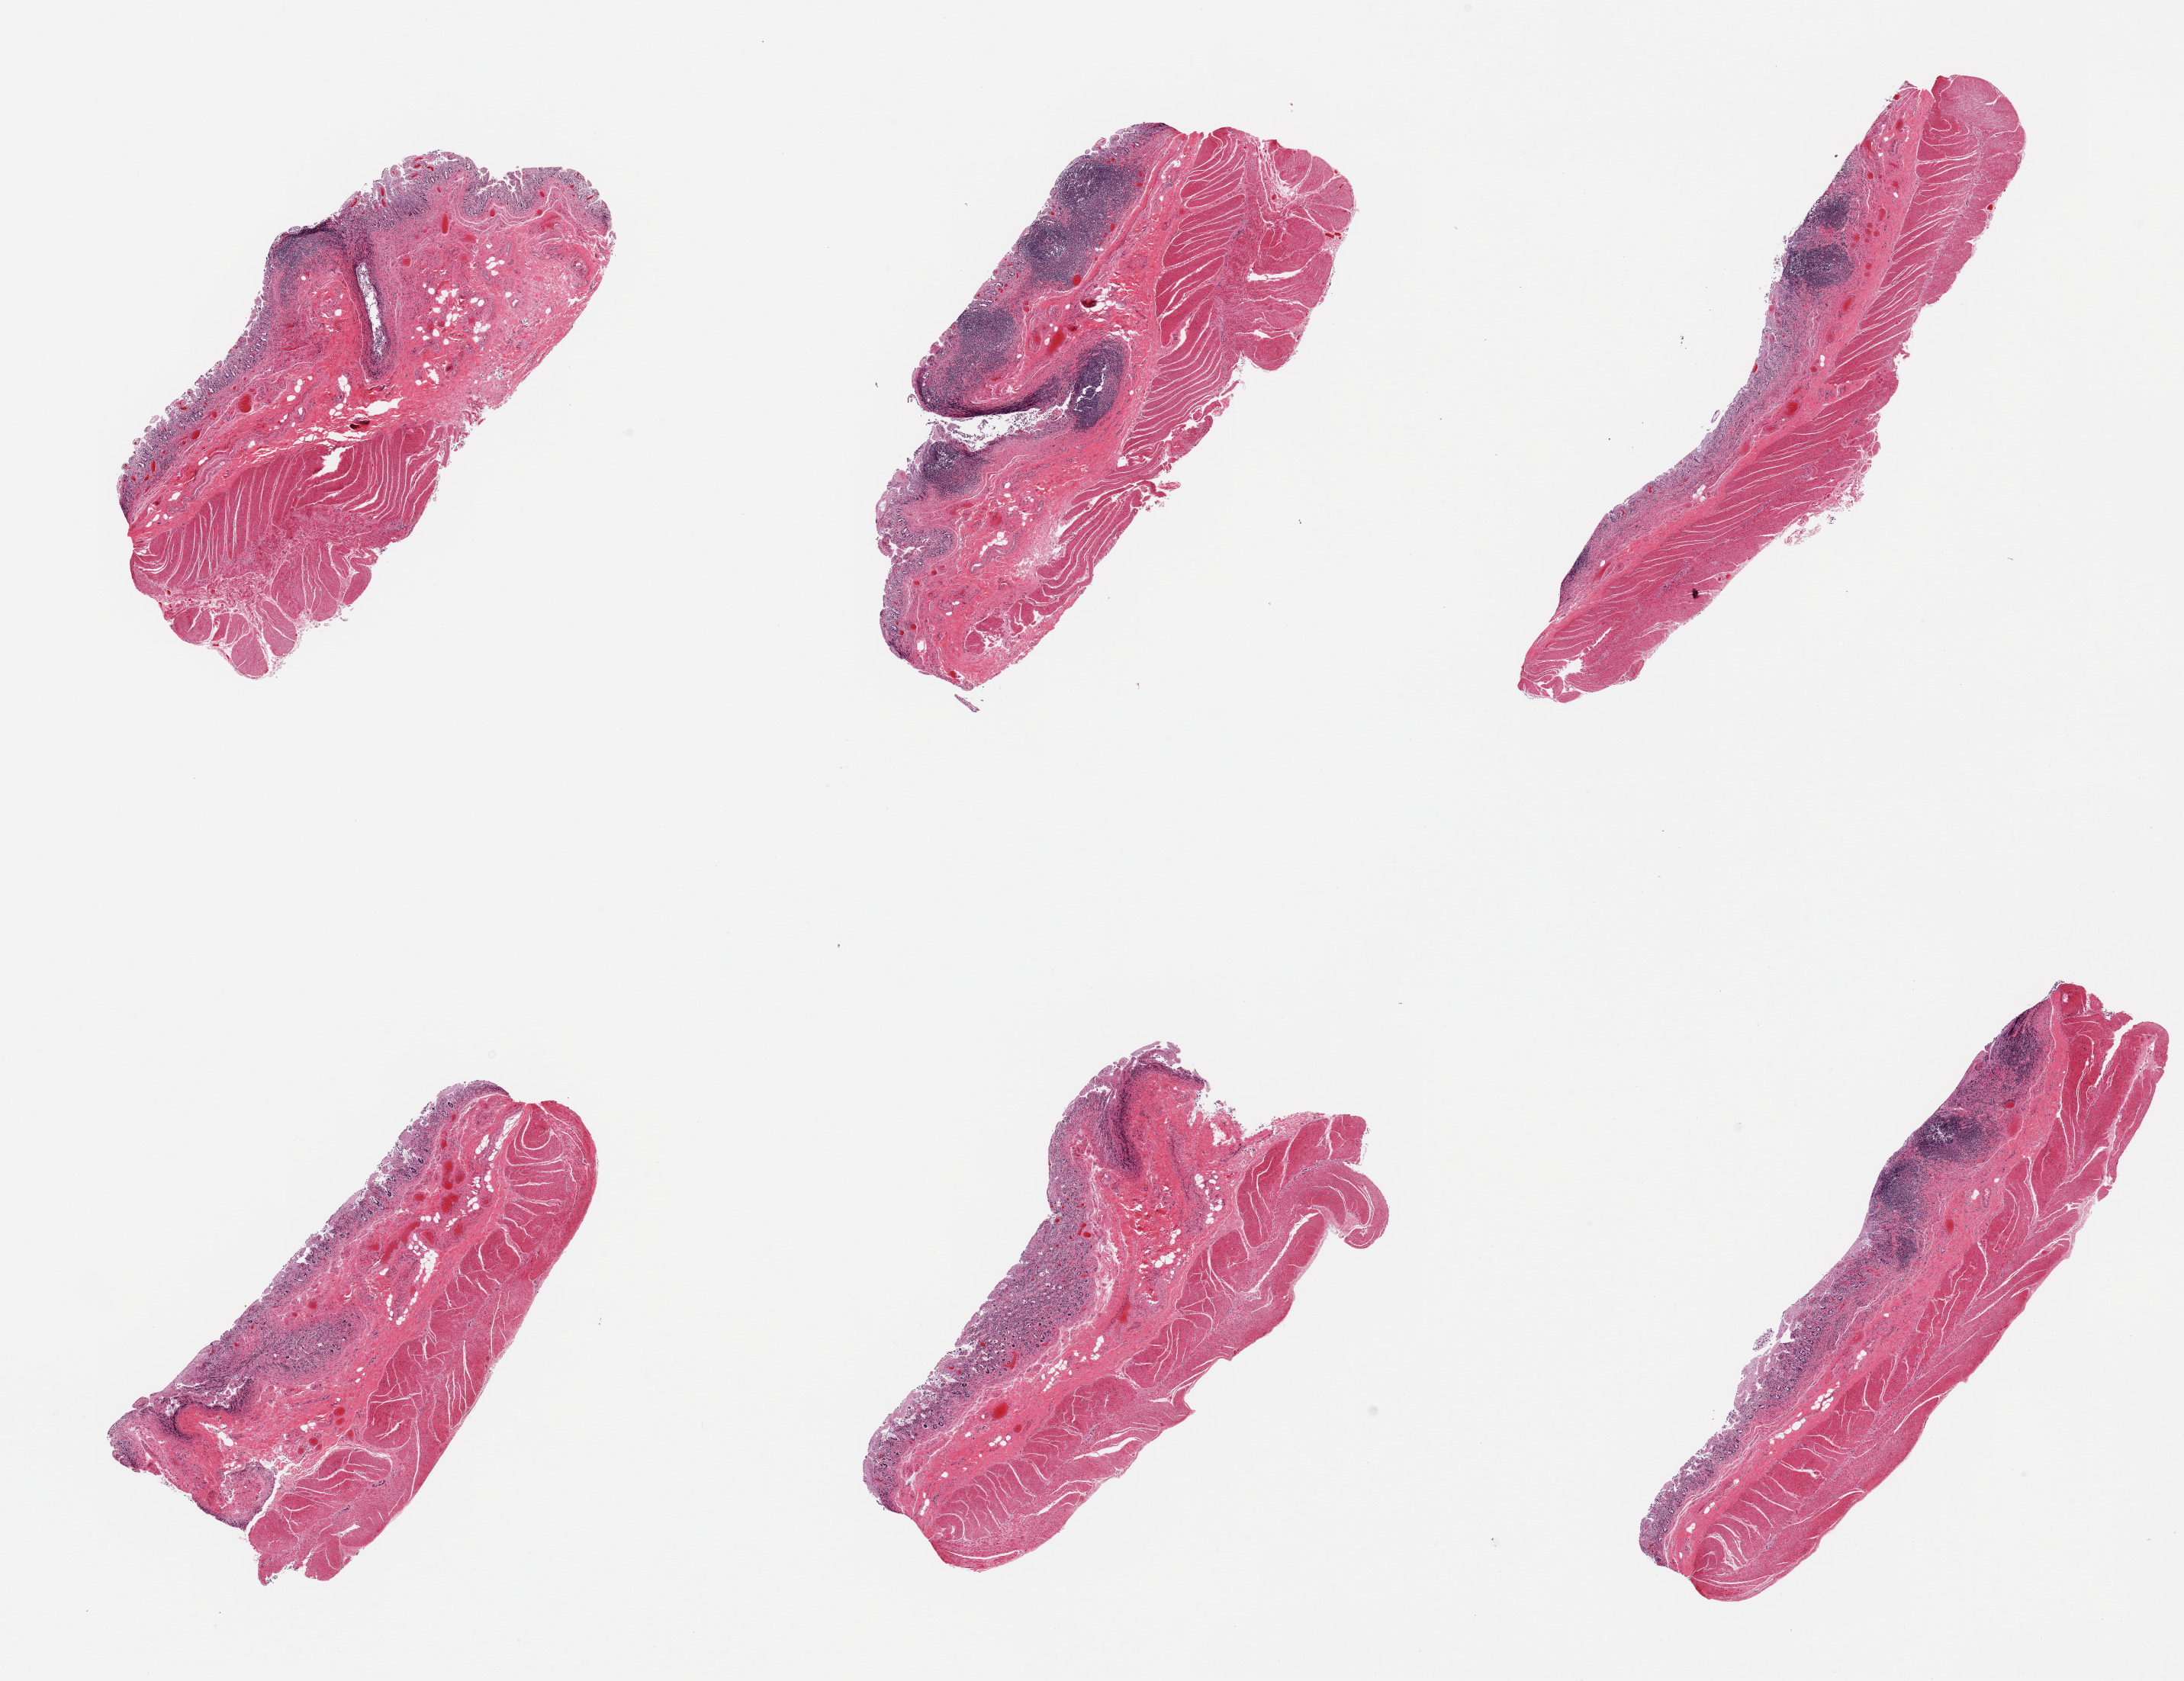
Digitized H&E-stained section — shown as a low-resolution overview of the whole scanned area (about 22.6 x 17.4 mm, from a 20x scan). PAXgene-fixed, paraffin-embedded tissue. Target tissue: transverse colon. Tissue donor sample. Donor: male.
Pathologist's review note for this sample: 6 pieces; grade 3 autolyzed mucosa; preserved muscularis; congestion; prominent lymphoid aggregates.